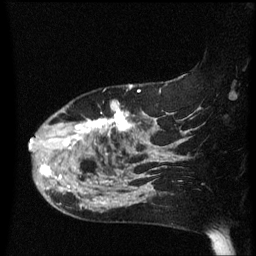
Breast MRI (dynamic contrast-enhanced), one sagittal slice; position 46 of 60 along the scan axis; dynamic contrast-enhanced series, image 2 of 3 at this slice position (ordered by acquisition); 1.5 T; TE 4.2 ms, TR 8.4 ms; 2.2 mm slice thickness; 256 × 256 image matrix. Female patient, age 47 years.
Structures marked on this image (semi-automatically segmented with operator editing):
- analysis volume of interest (the breast-tissue region the enhancement analysis was run in; not a lesion): bounding box <30,102,149,206> (left, top, right, bottom; pixels)
- tumour enhancement mask (voxels above the 70 % enhancement threshold inside the analysis volume of interest): <30,102,135,204>